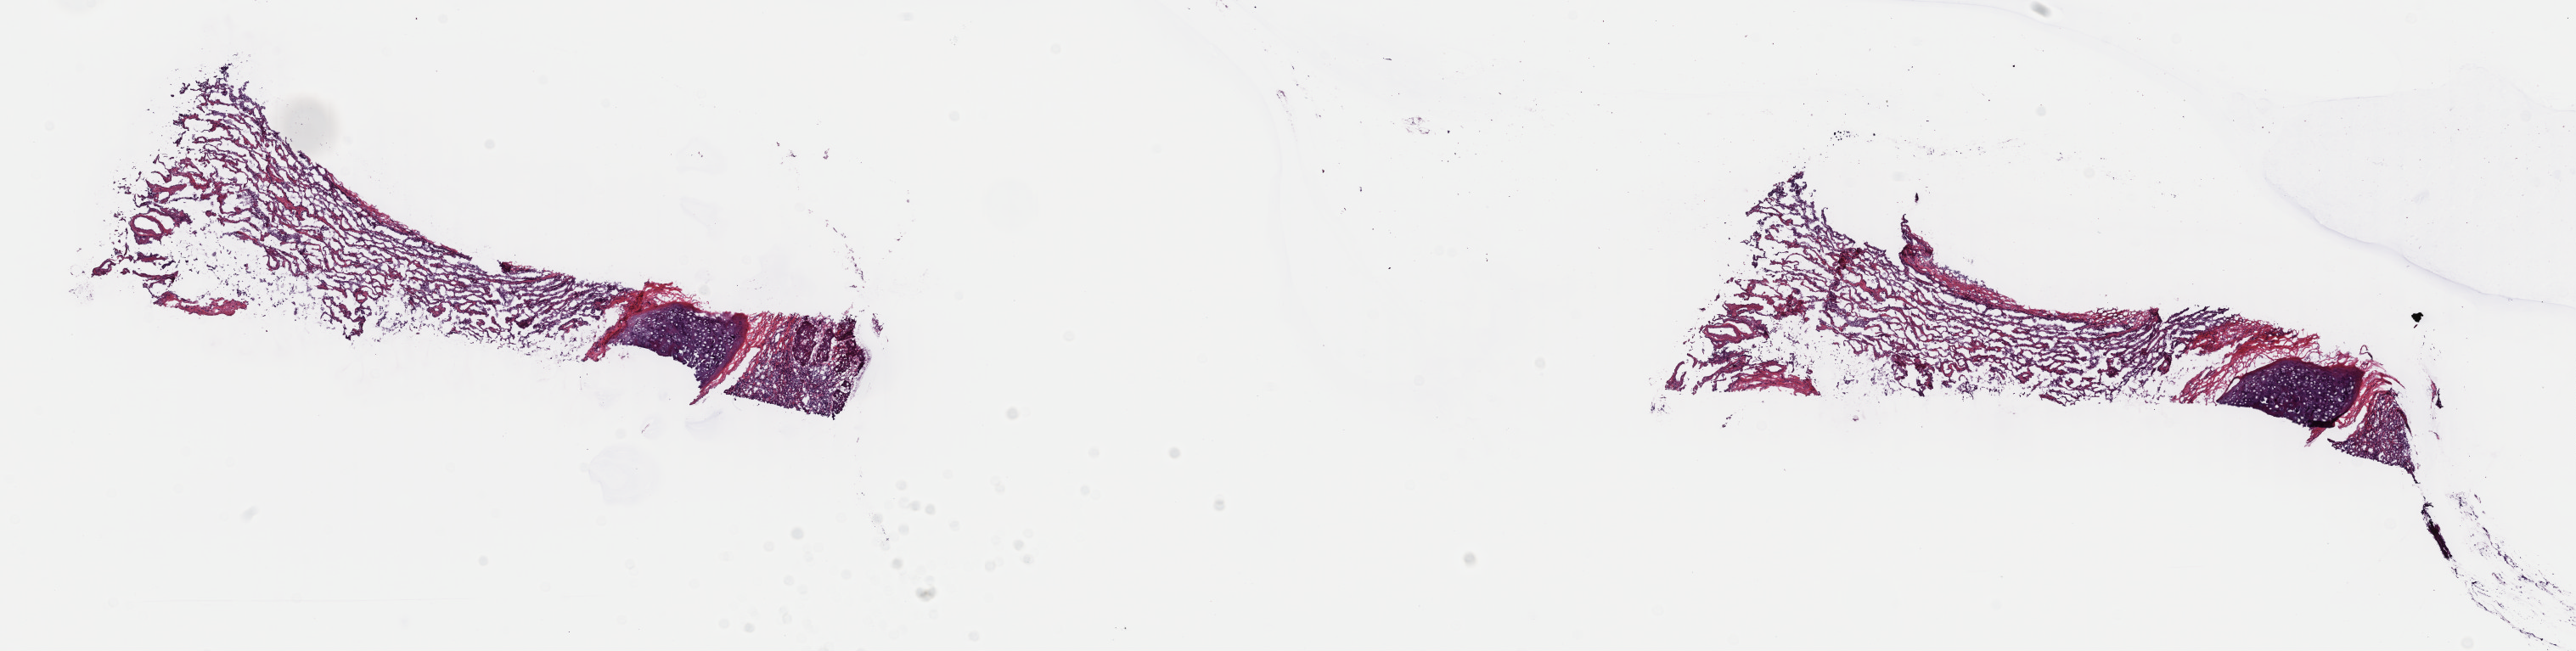
Whole-slide histology image, H&E-stained, low-resolution overview of the scanned area, about 23.9 x 6.1 mm (acquisition: 40x scan); frozen section from the top of the tissue portion; primary tumour sample from the lung. Male patient; age at initial diagnosis 68 years. Pathologist review of this section (percent, as recorded): tumour cells 60%, tumour nuclei 60%, normal cells 20%, stromal cells 10%, necrosis 10%. Inflammatory infiltration, as recorded: lymphocyte infiltration 40%, monocyte infiltration 20%, neutrophil infiltration 20%.
TNM: T2a N0 M0. AJCC pathologic stage: IB. Diagnosis: Squamous cell carcinoma, keratinizing, NOS (lower lobe, lung).